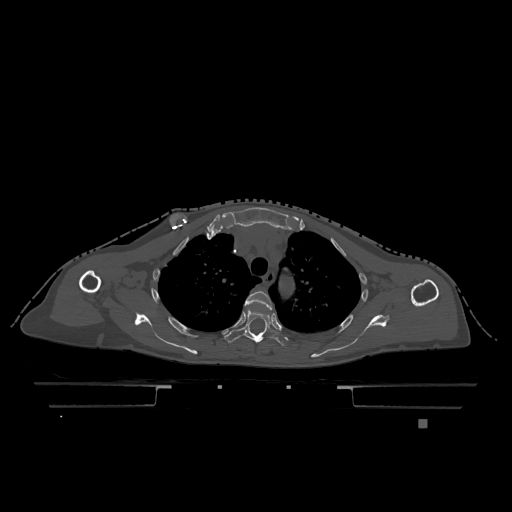
CT including the spine, one axial slice; slice 893 of 1317 in the series (ordered by position); bone window (W 1800 / L 400 HU); 0.5 mm slice thickness; 512 × 512 image matrix. Female patient, age 74 years. Case-level facts recorded for this patient, not image findings: primary cancer: lung; vertebrae with lytic lesions (as recorded): T1, T4, T5, T6, L4, L5.
Structures marked on this image (semi-automatically segmented with operator editing):
- T3 vertebra: bounding box [x1, y1, x2, y2] px = [245, 291, 273, 310]
- T4 vertebra: [224, 308, 289, 347]